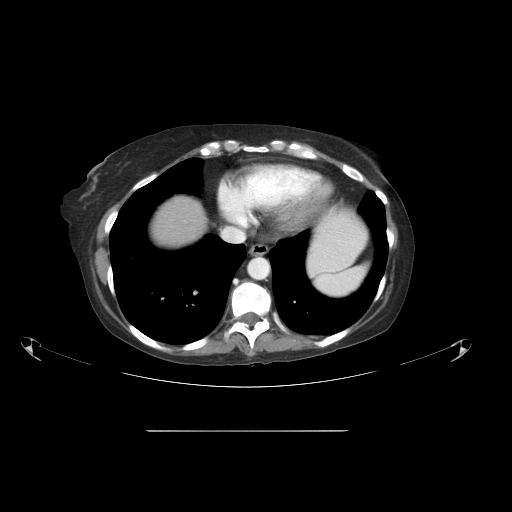
Contrast-enhanced abdominal CT, one axial slice; position 46 of 51 along the scan axis; intravenous contrast given; soft-tissue window (W 400 / L 40 HU); 5 mm slice thickness; 512 × 512 image matrix. Female patient, age 48 years. Case-level facts recorded for this patient, not image findings: diagnosis: colorectal cancer liver metastases, imaged before liver resection; multiple liver metastases: yes; largest metastasis: 1 cm.
Outlined on this slice (expert manual segmentation):
- liver: bounding box [x1, y1, x2, y2] px = [150, 198, 207, 248]
- planned liver remnant (the part of the liver to remain after resection): [151, 197, 206, 248]